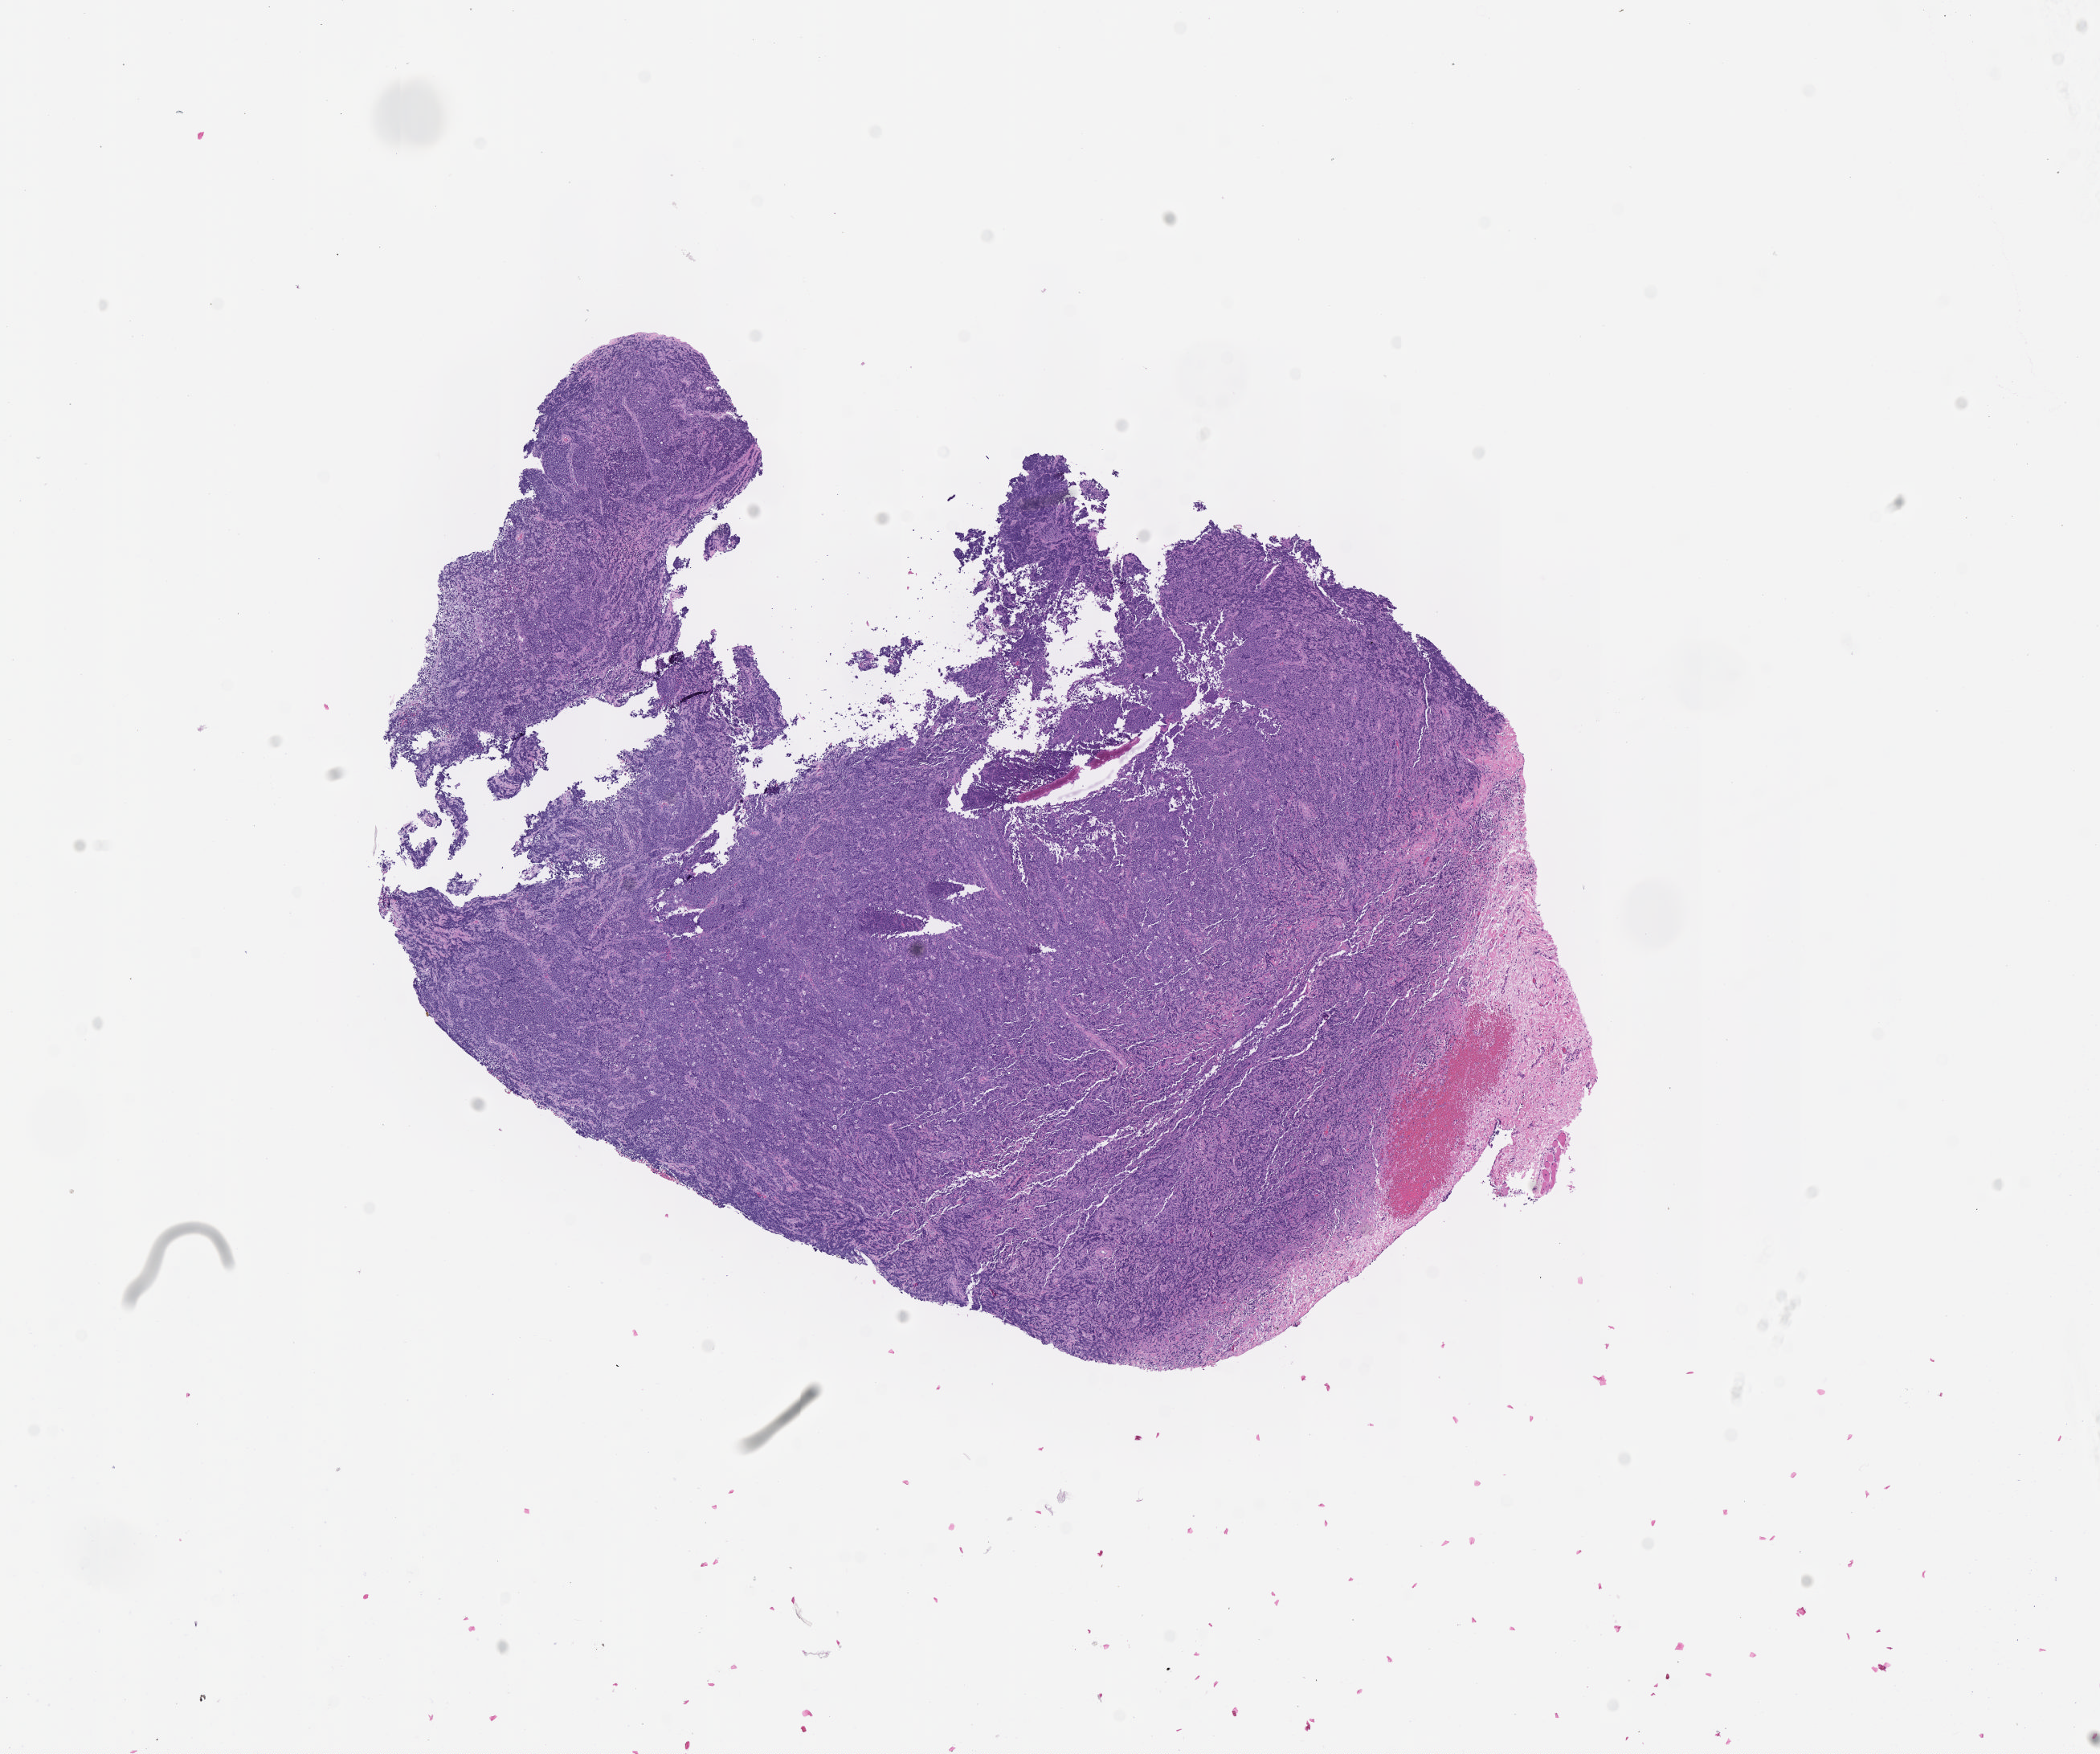
Digitized H&E-stained section — a low-resolution overview of the entire scanned area, about 10.6 x 8.8 mm, specimen: tumor tissue, site: mandible. Female patient; age at initial diagnosis 7 years.
Histologic diagnosis: Burkitt lymphoma, NOS.